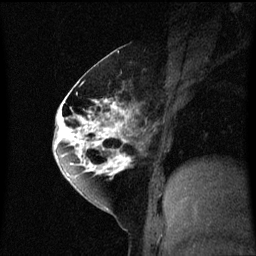
Breast MRI (dynamic contrast-enhanced), one sagittal slice; slice 29 of 60 in the series (ordered by position); dynamic contrast-enhanced series, image 2 of 3 at this slice position (ordered by acquisition); 1.5 T; TE 4.2 ms, TR 8.4 ms; 256 × 256 image matrix, field of view 200 × 200 mm. Patient: female, 60 years.
Outlined on this slice (semi-automatically segmented with operator editing):
- analysis volume of interest (the breast-tissue region the enhancement analysis was run in; not a lesion): bounding box [x1, y1, x2, y2] px = [64, 70, 139, 195]
- tumour enhancement mask (voxels above the 70 % enhancement threshold inside the analysis volume of interest): [64, 76, 139, 187]